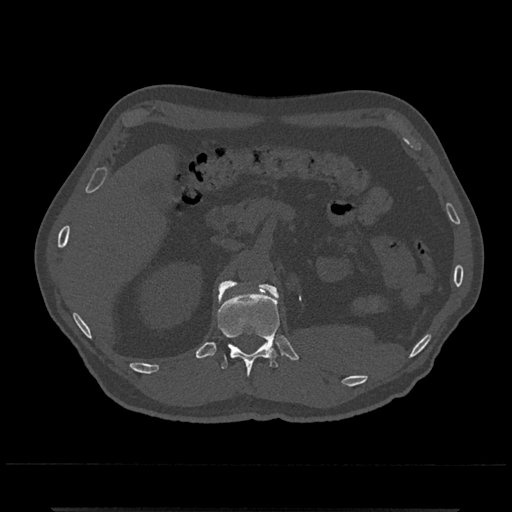
CT including the spine, one axial slice; slice 420 of 797 in the series (ordered by position); reconstruction kernel Br40s/3; bone window (W 1800 / L 400 HU); 0.5 mm slice thickness; 512 × 512 image matrix, field of view 393 × 393 mm. Patient: male, 67 years. From the clinical record (not read from this slice): primary cancer: prostate.
Annotated regions visible in this slice (semi-automatic segmentation, software-assisted and operator-edited):
- L1 vertebra: bounding box <219,282,277,296> (left, top, right, bottom; pixels)
- T12 vertebra: <217,281,280,377>